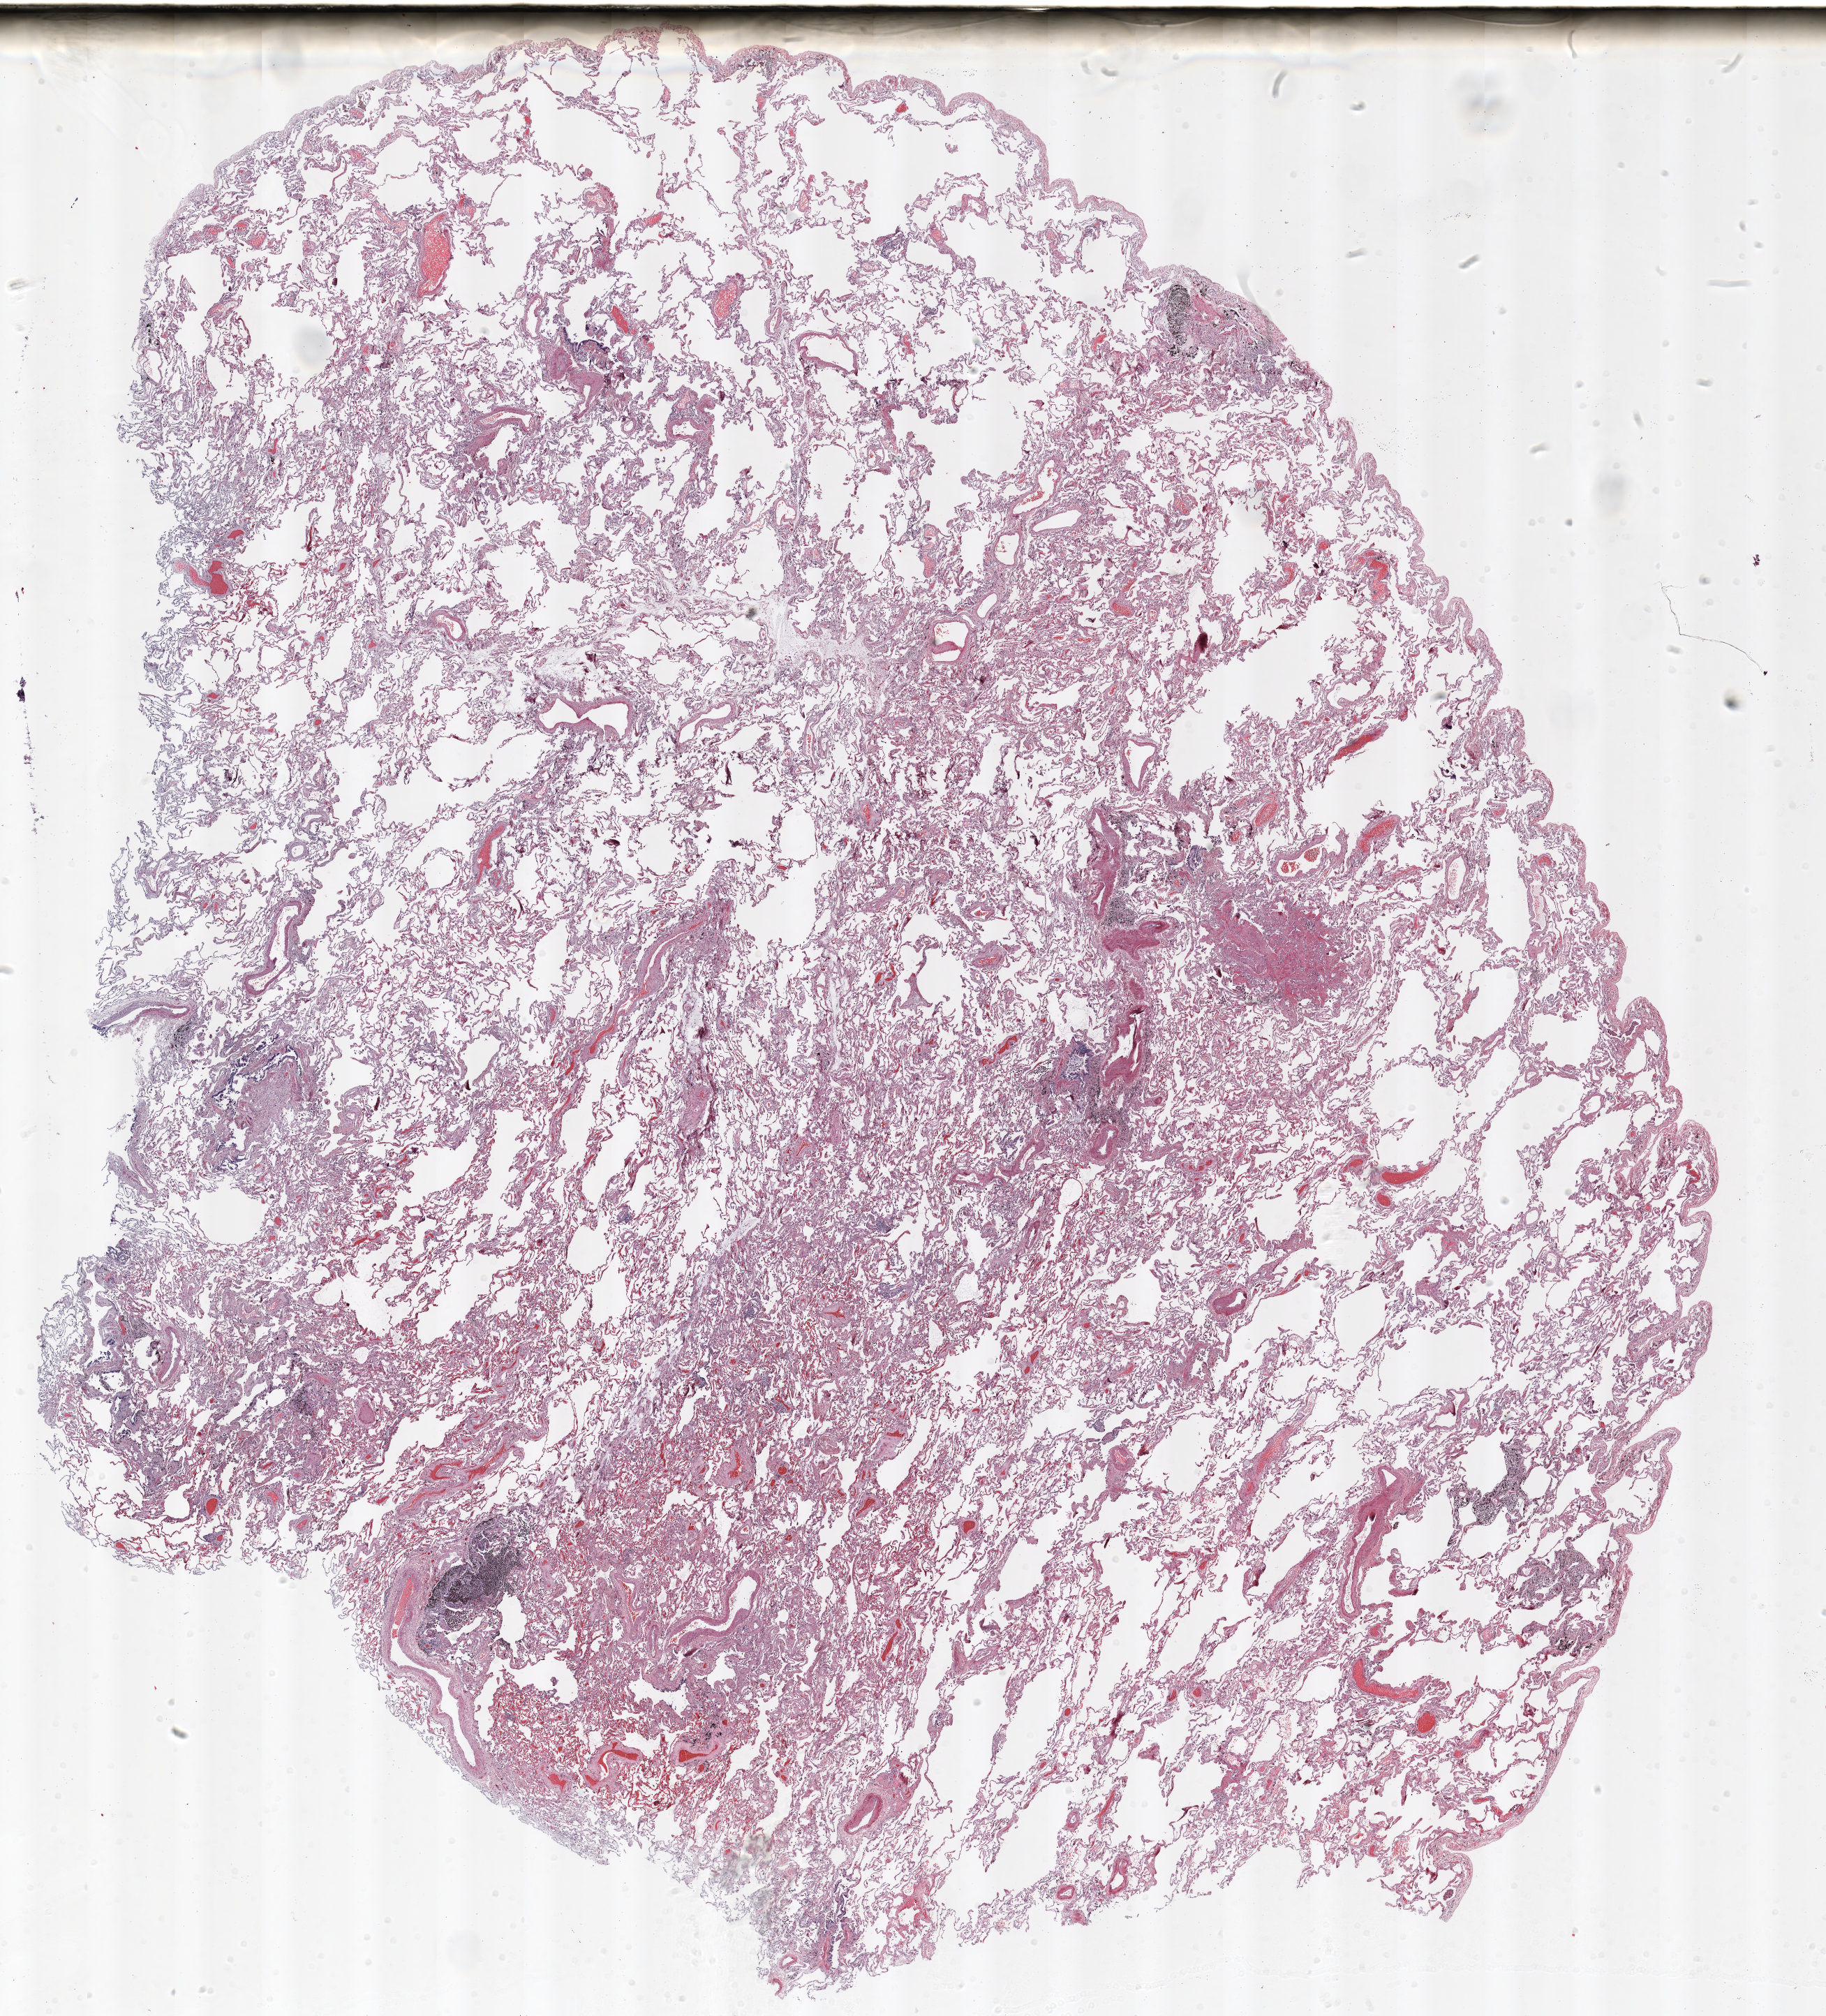
Whole-slide histology image, Hematoxylin and eosin (H&E) stained — shown as a low-resolution overview of the whole scanned area (about 21.0 x 23.2 mm, slide scanned at 20x), FFPE section, lung tissue. Male patient, aged 72 at enrolment. Current smoker at enrolment. Grade: moderately differentiated (G2).
Stage (AJCC 6th edition): IB. Participant's lung-cancer diagnosis: Adenocarcinoma, NOS. Tumour size (pathology): 30 mm. Primary tumour location (clinical record): right upper lobe.